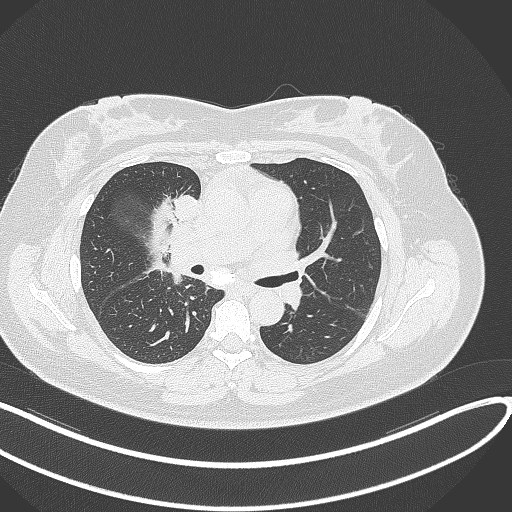
Chest CT, one axial slice; slice 154 of 303 in the series (ordered by position); reconstruction kernel B70f; 120 kVp; lung window (W 1500 / L -600 HU); 1 mm slice thickness; 512 × 512 image matrix. Female patient, age 46 years. Case-level facts recorded for this patient, not image findings: clinical TNM (as recorded): T2a N1 M0.
Outlined on this slice (bounding box drawn by a radiologist):
- lung tumour (recorded histology: adenocarcinoma): bounding box [x1, y1, x2, y2] px = [174, 192, 202, 225]